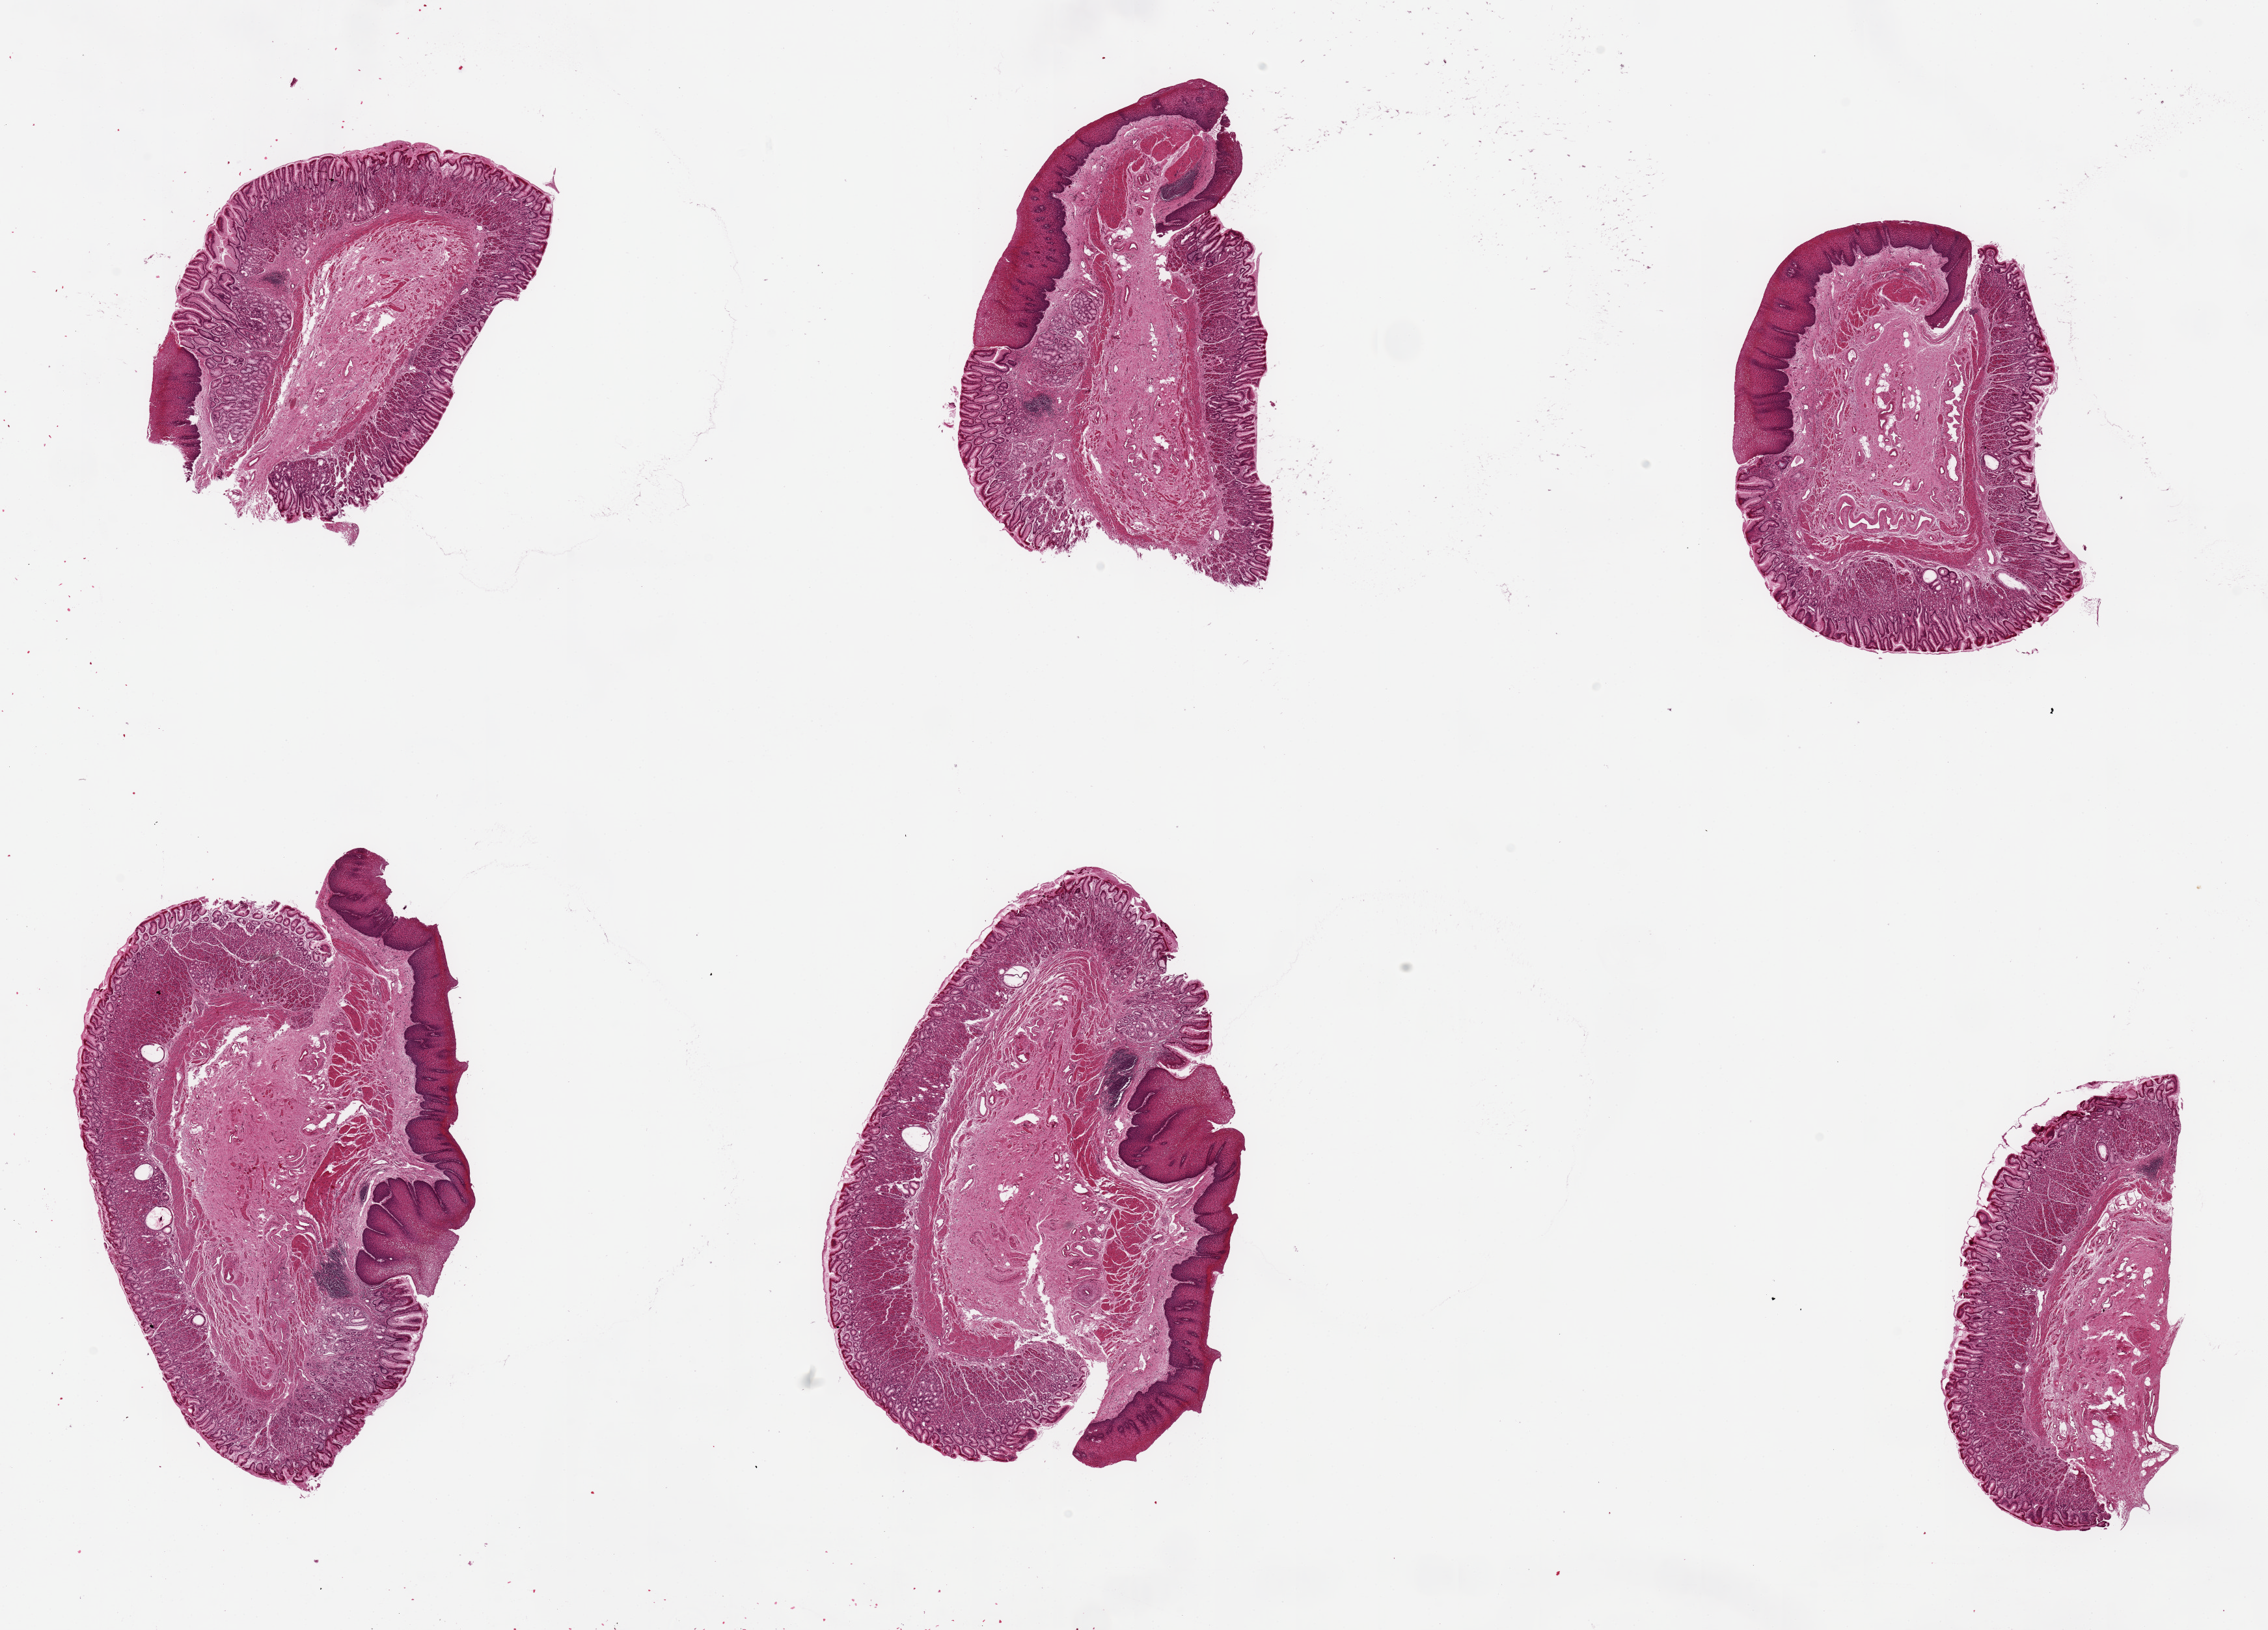
Hematoxylin and eosin (H&E) whole-slide image, low-resolution overview of the scanned area, about 27.6 x 19.8 mm; PAXgene-fixed, paraffin-embedded tissue; sampled site (target tissue): esophageal mucous membrane; donor tissue sample. Donor: male.
Reviewer comment on this tissue sample: 6 pieces, up to 8x5mm; 5 with squamous and glandular mucosa; 1 all glandular.